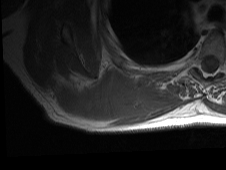
MRI of an extremity soft-tissue mass, one axial slice. Position 24 of 81 along the scan axis. MR volume resampled by the dataset authors to the PET/CT grid (not the native acquisition matrix). 226 × 170 image matrix. Male patient. Case-level facts recorded for this patient, not image findings: histological type: pleiomorphic spindle cell undifferentiated; grade: high; site of the primary tumour: right parascapusular.
Annotated regions visible in this slice (expert contour drawn on MRI and transferred to this co-registered scan by the dataset authors):
- gross tumour volume including surrounding oedema: bounding box <46,70,180,126> (left, top, right, bottom; pixels)
- gross tumour volume (mass): <58,72,143,121>